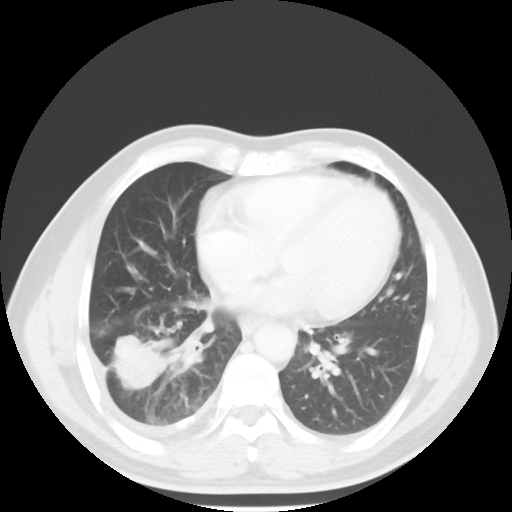
Chest CT, one axial slice. Slice 22 of 56 in the series (ordered by position). Reconstruction kernel STANDARD. 120 kVp. Lung window (W 1500 / L -600 HU). 512 × 512 image matrix, field of view 344 × 344 mm. Male patient, age 56 years. Case-level facts recorded for this patient, not image findings: clinical TNM (as recorded): T2 N3 M1.
Outlined on this slice (rectangle marked by the reading radiologist):
- lung tumour (recorded histology: adenocarcinoma): bounding box [x1, y1, x2, y2] px = [110, 330, 175, 392]